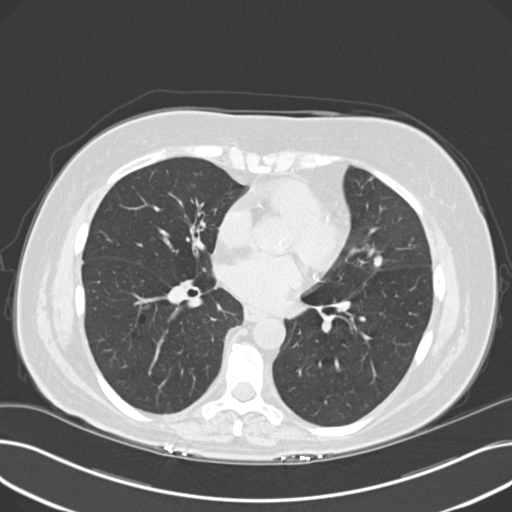
Low-dose screening chest CT, one axial slice; position 91 of 203 along the scan axis; 120 kVp; lung window (W 1500 / L -600 HU); 2 mm slice thickness; 512 × 512 image matrix.
Annotated regions visible in this slice (expert manual segmentation):
- lesion 1 (tumor, upper lobe of left lung): bounding box <374,255,384,268> (left, top, right, bottom; pixels)